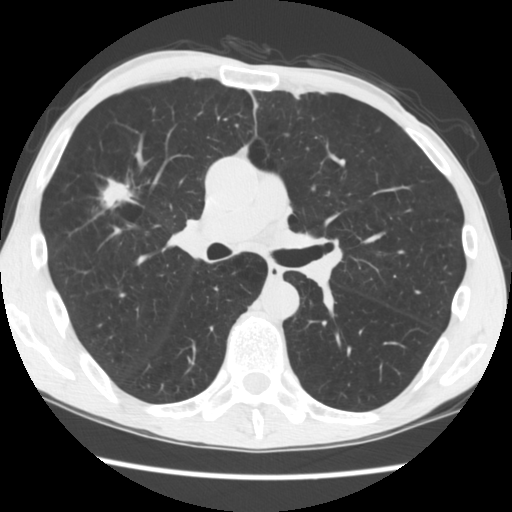
Low-dose screening chest CT, one axial slice; position 102 of 181 along the scan axis; reconstruction kernel STANDARD; lung window (W 1500 / L -600 HU); 2.5 mm slice thickness; 512 × 512 image matrix, field of view 330 × 330 mm.
Annotated regions visible in this slice (outlined manually by an expert reader):
- lesion 1 (tumor, upper lobe of right lung): bounding box [x1, y1, x2, y2] px = [99, 178, 134, 209]